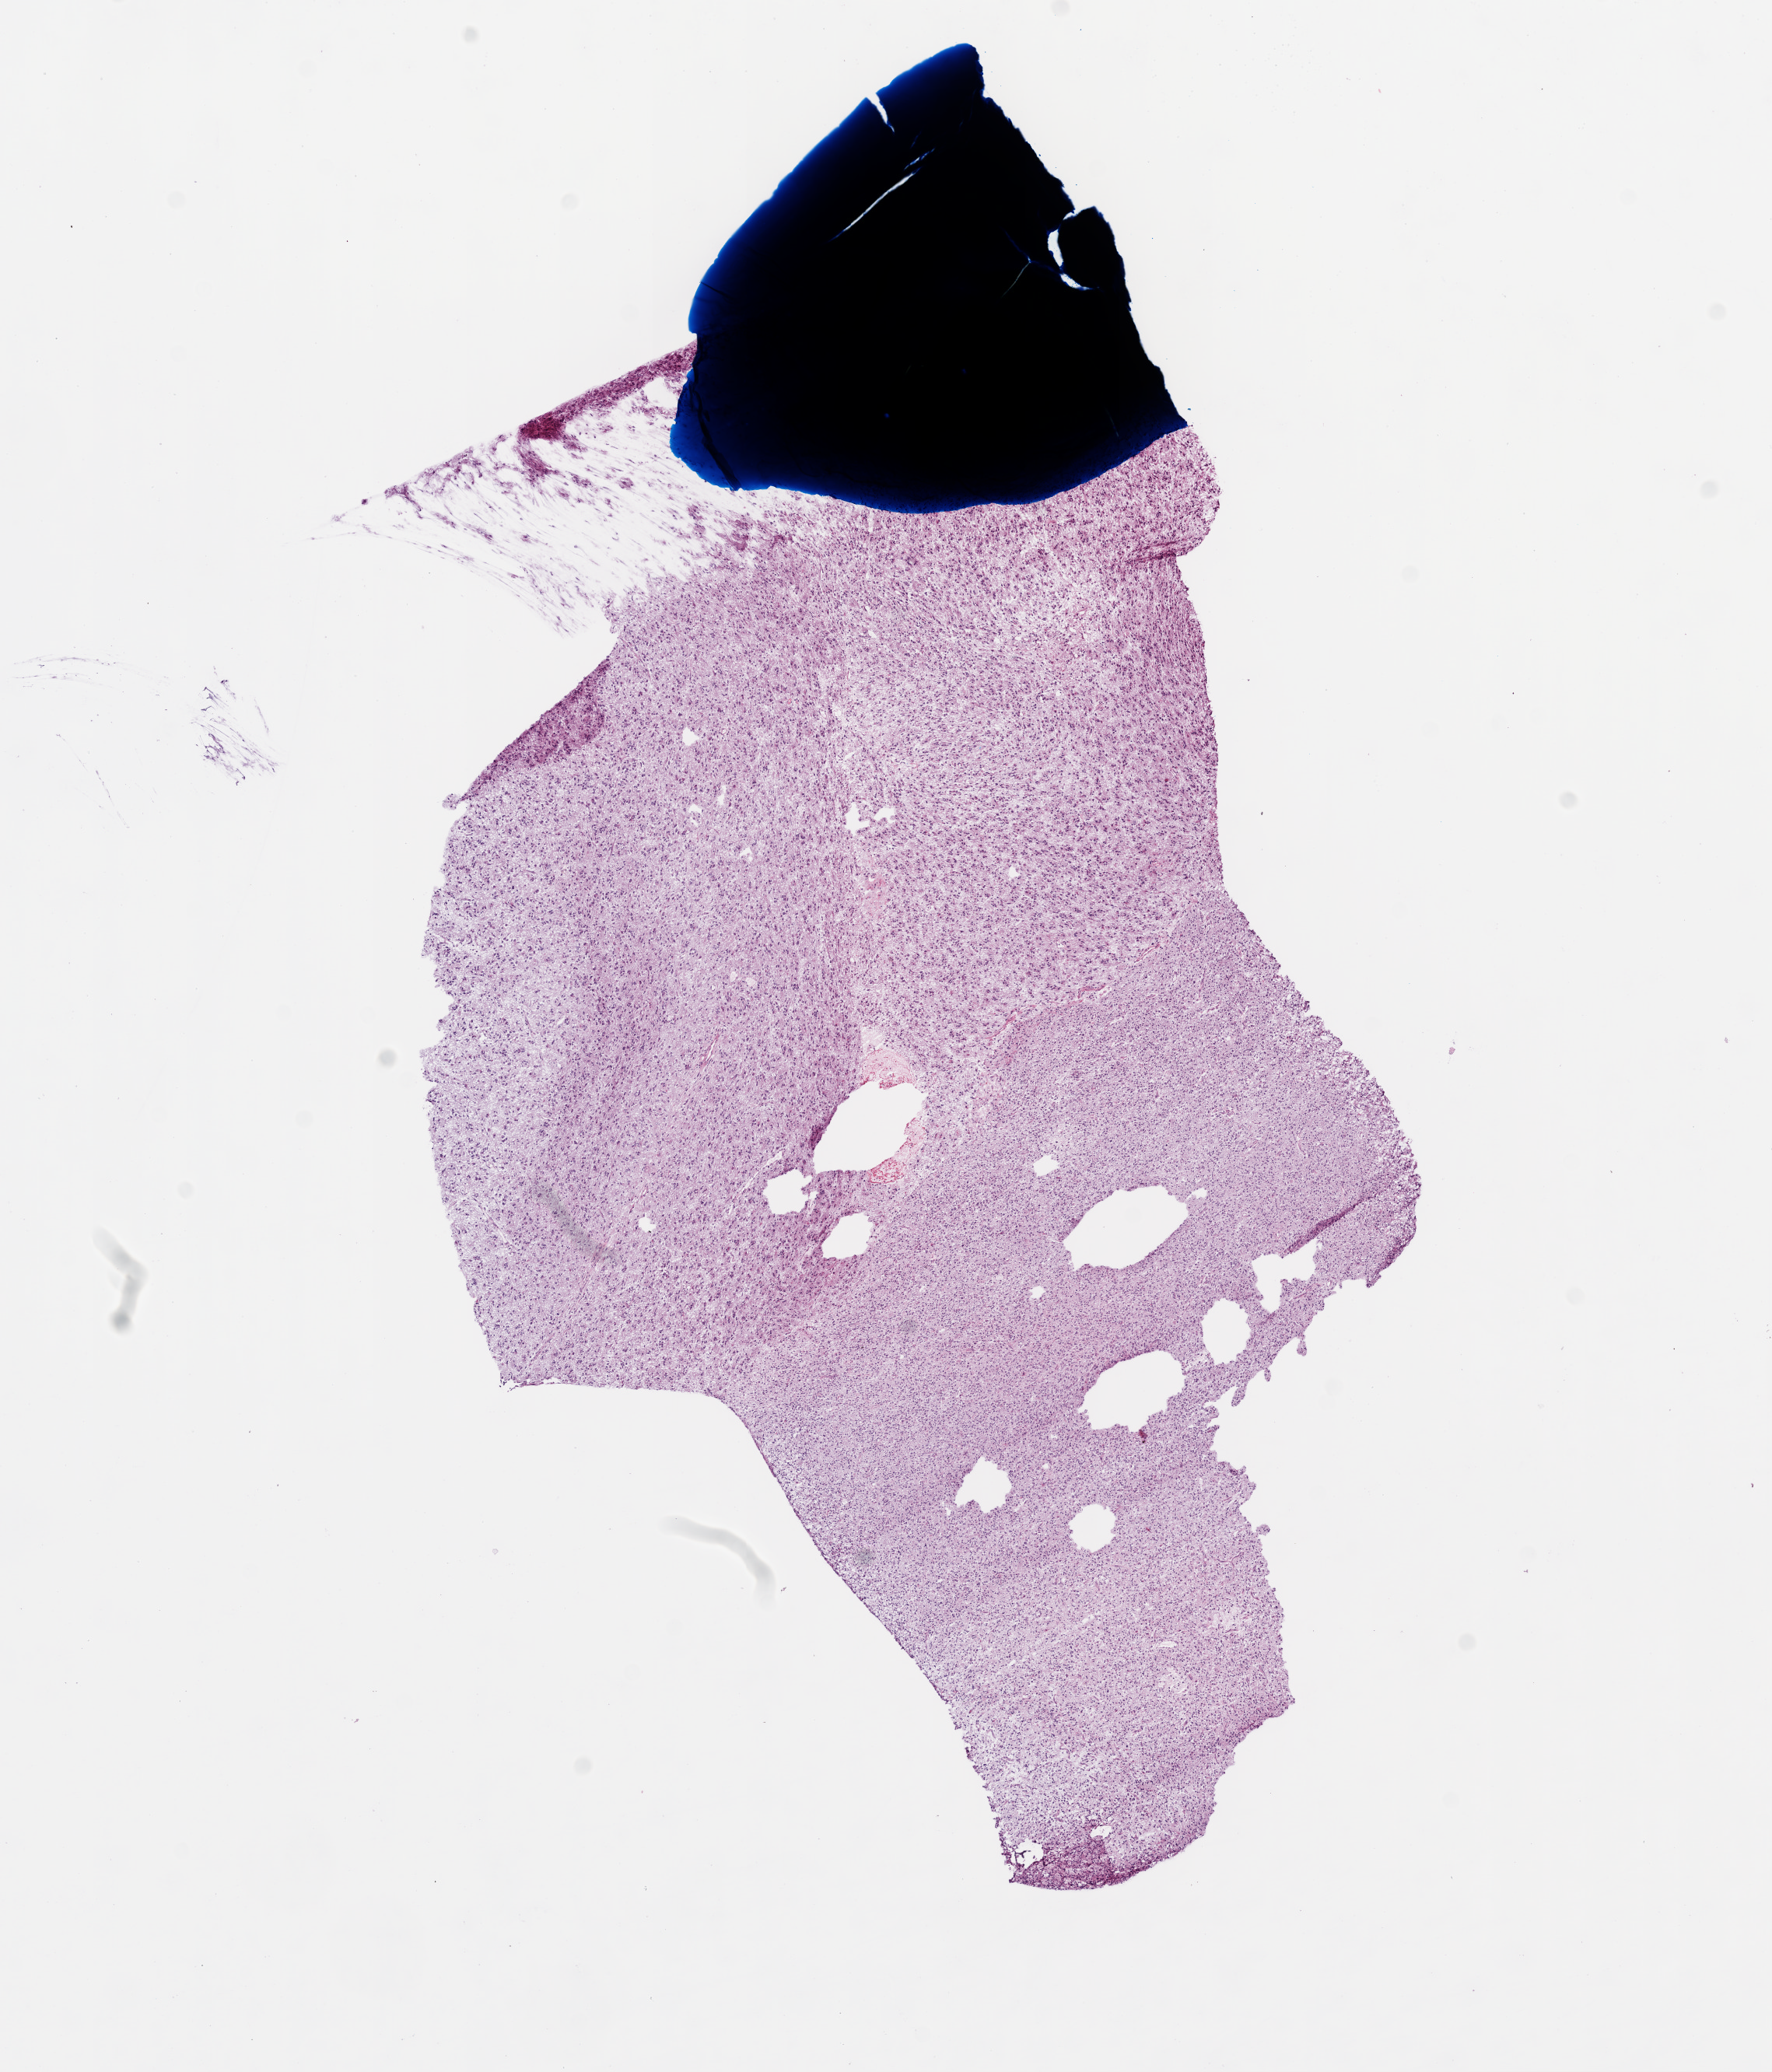
Digitized Hematoxylin and eosin (H&E) stained tissue section (whole slide), shown as a low-resolution overview of the whole scanned area (about 9.2 x 10.7 mm, from a 20x scan), frozen section from the top of the tissue portion, brain, primary tumour sample. Male, age 69 years at initial diagnosis. Composition of this section per pathologist review: tumour cells 95%, tumour nuclei 100%.
Pathologic diagnosis: Glioblastoma.